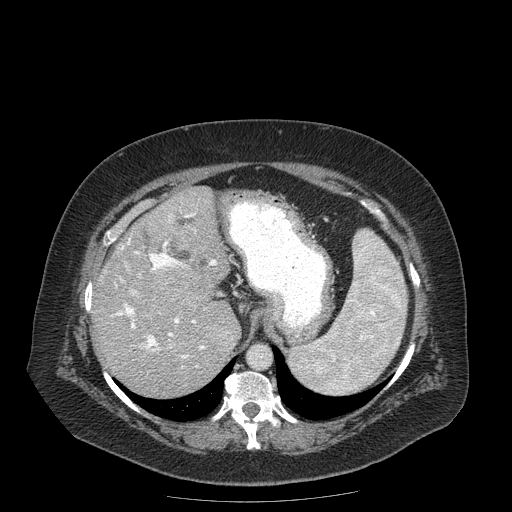
Contrast-enhanced abdominal CT (liver protocol), one axial slice; position 127 of 204 along the scan axis; reconstruction kernel STANDARD; 120 kVp; soft-tissue window (W 400 / L 40 HU); 512 × 512 image matrix, field of view 440 × 440 mm. From the clinical record (not read from this slice): diagnosis: hepatocellular carcinoma (patient treated with transarterial chemoembolisation; whether this scan precedes or follows treatment is not stated here); TNM stage (as recorded): Stage-IIIB; Child-Pugh class: A; tumour differentiation: well differentiated; tumour nodularity: uninodular.
Outlined on this slice (semi-automatically segmented with operator editing):
- abdominal aorta: box from (x=248, y=345) to (x=271, y=368) px
- liver parenchyma outside the tumour (the mass and vessels are separate outlines, so this box may not span the whole liver): (x=92, y=186)–(x=240, y=396)
- mass: (x=150, y=266)–(x=211, y=316)
- liver vessels: (x=111, y=212)–(x=228, y=368)